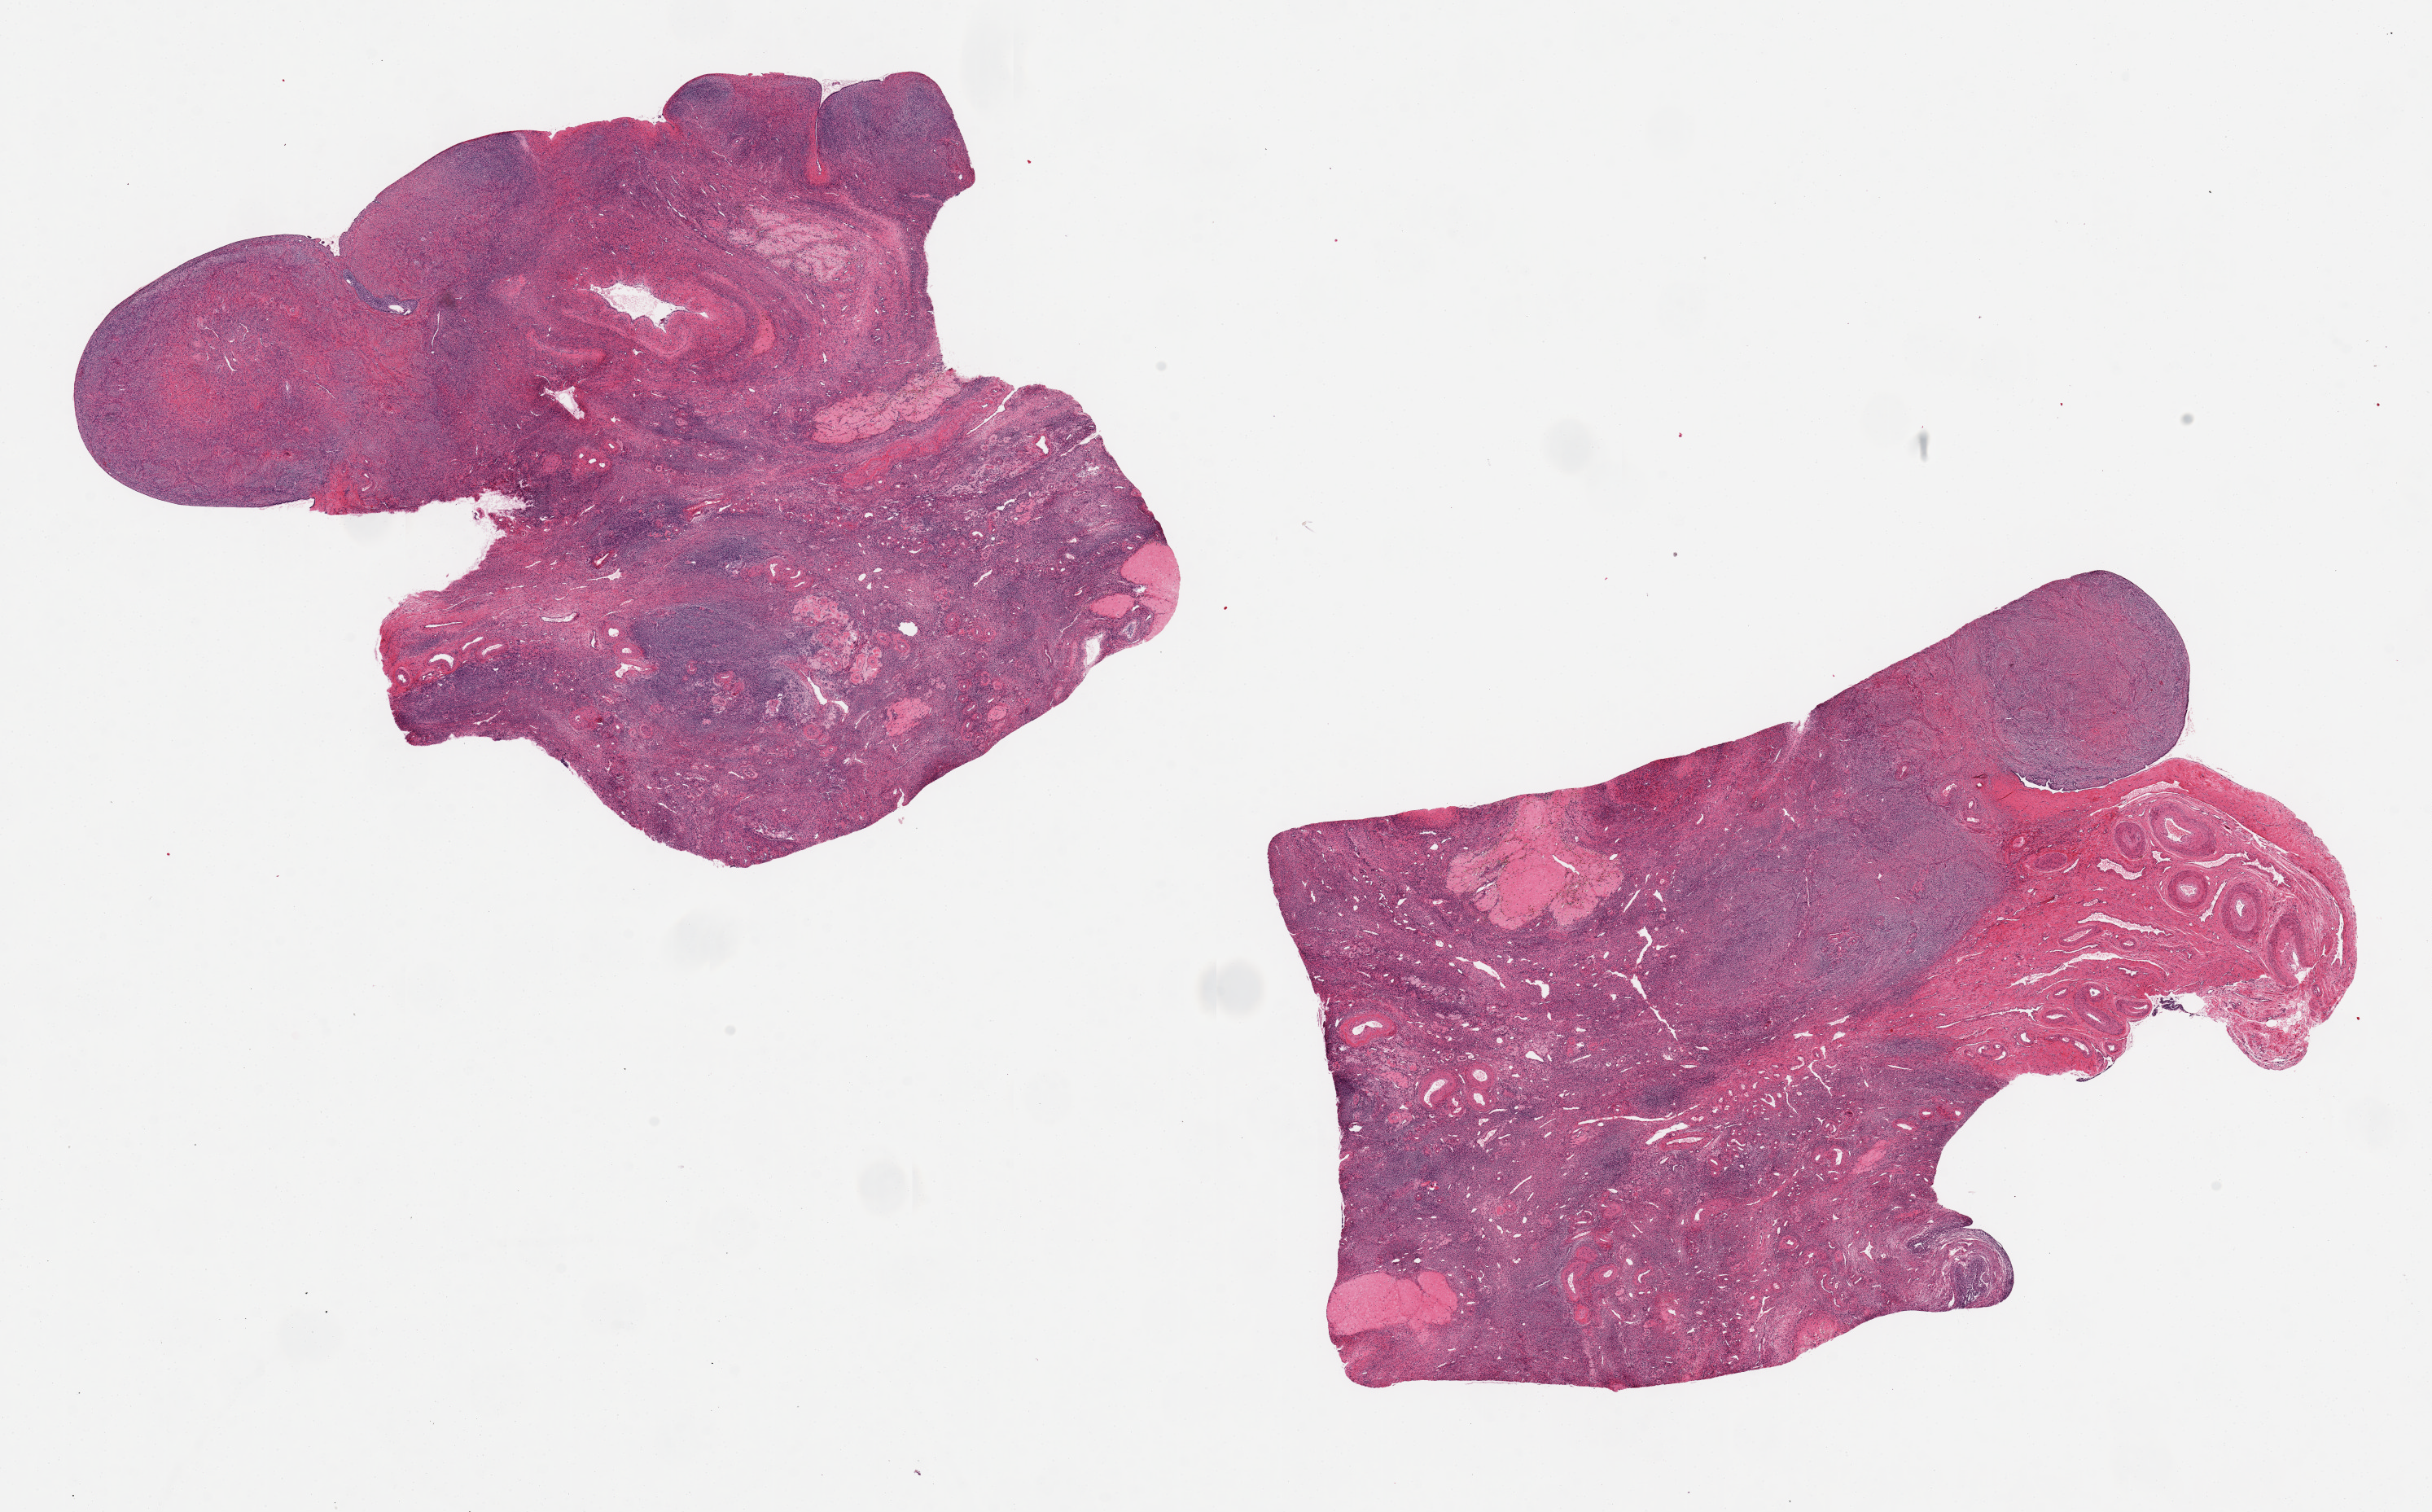
Hematoxylin and eosin (H&E) whole-slide image, shown as a low-resolution overview of the whole scanned area (about 23.6 x 14.7 mm); PAXgene-fixed, paraffin-embedded tissue; section of ovary (target tissue); tissue donor sample. Donor: female.
Pathologist's review note for this sample: 2 aliquots, ~9x6.5mm. Post-menopausal atrophic changes.